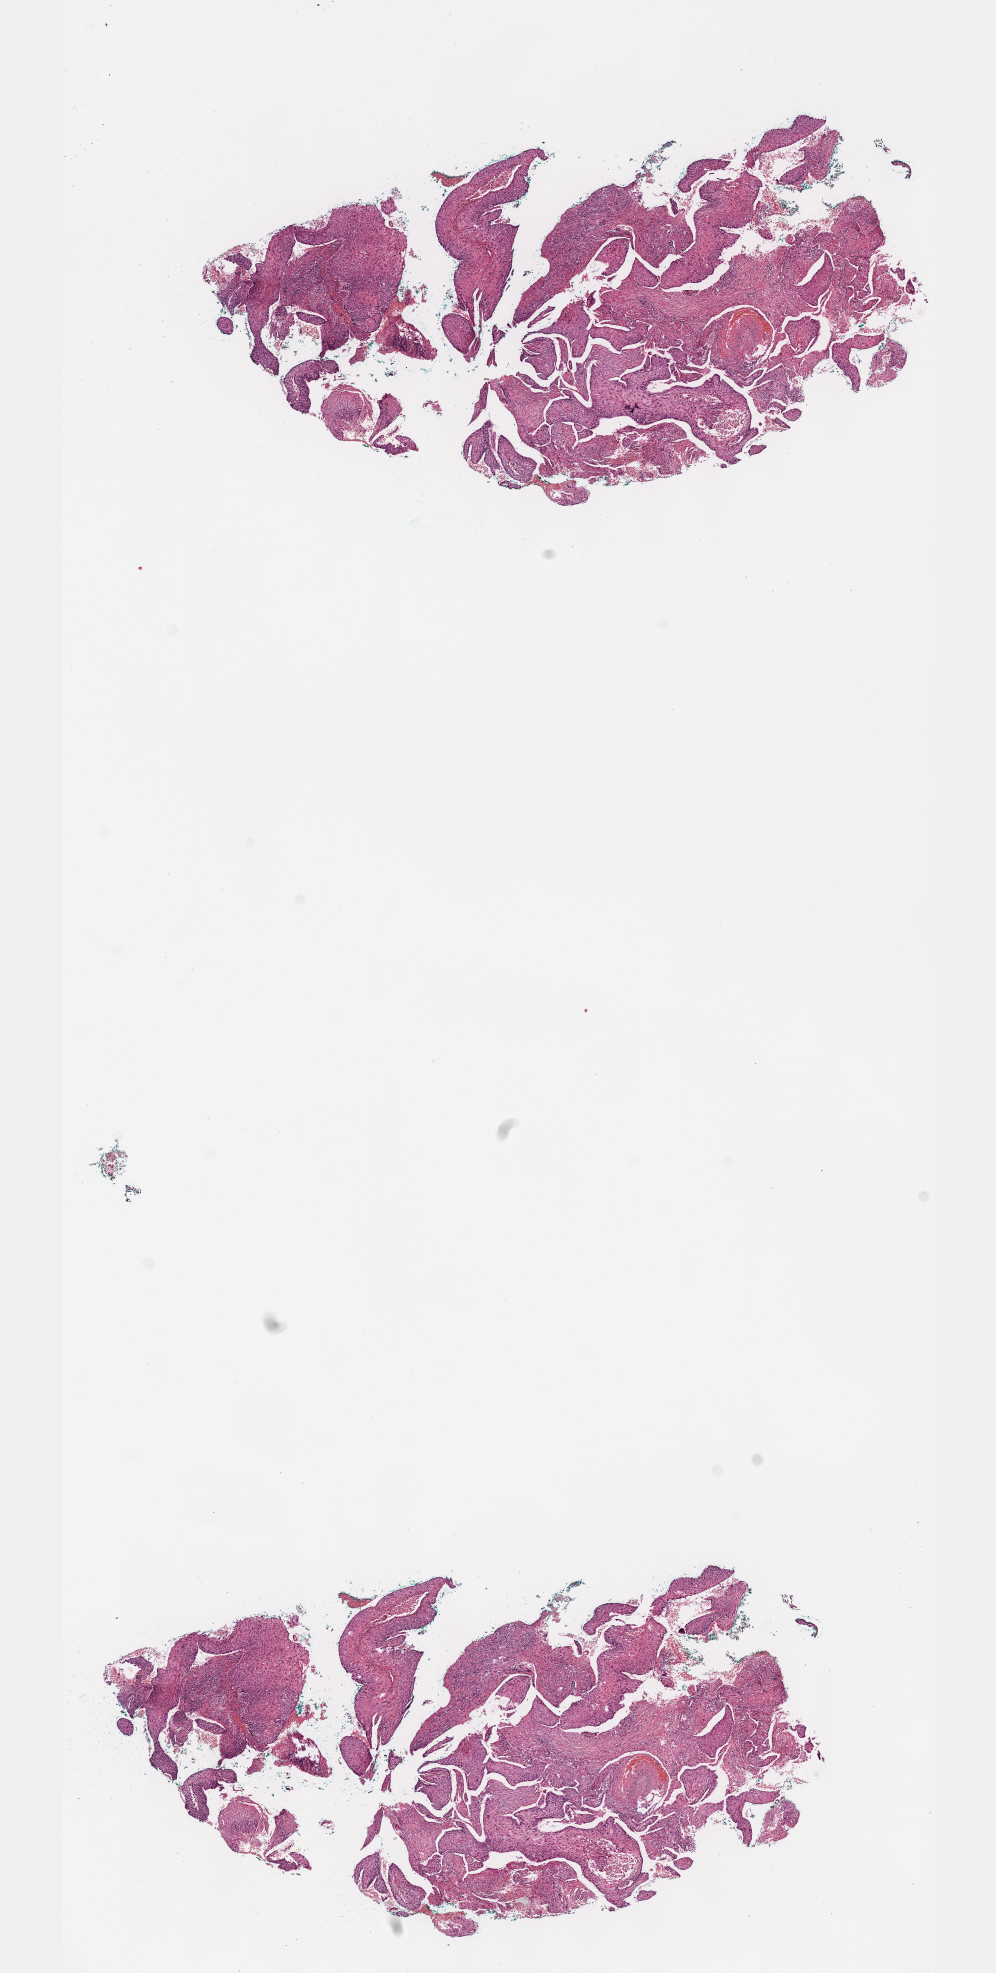
Digitized H&E-stained tissue section (whole slide) — whole scanned area (about 8.0 x 15.9 mm) shown as a low-resolution overview. FFPE section. Cervix, primary tumour sample. Female patient; age at initial diagnosis 47 years.
Histologic diagnosis: Squamous cell carcinoma, NOS (cervix uteri).